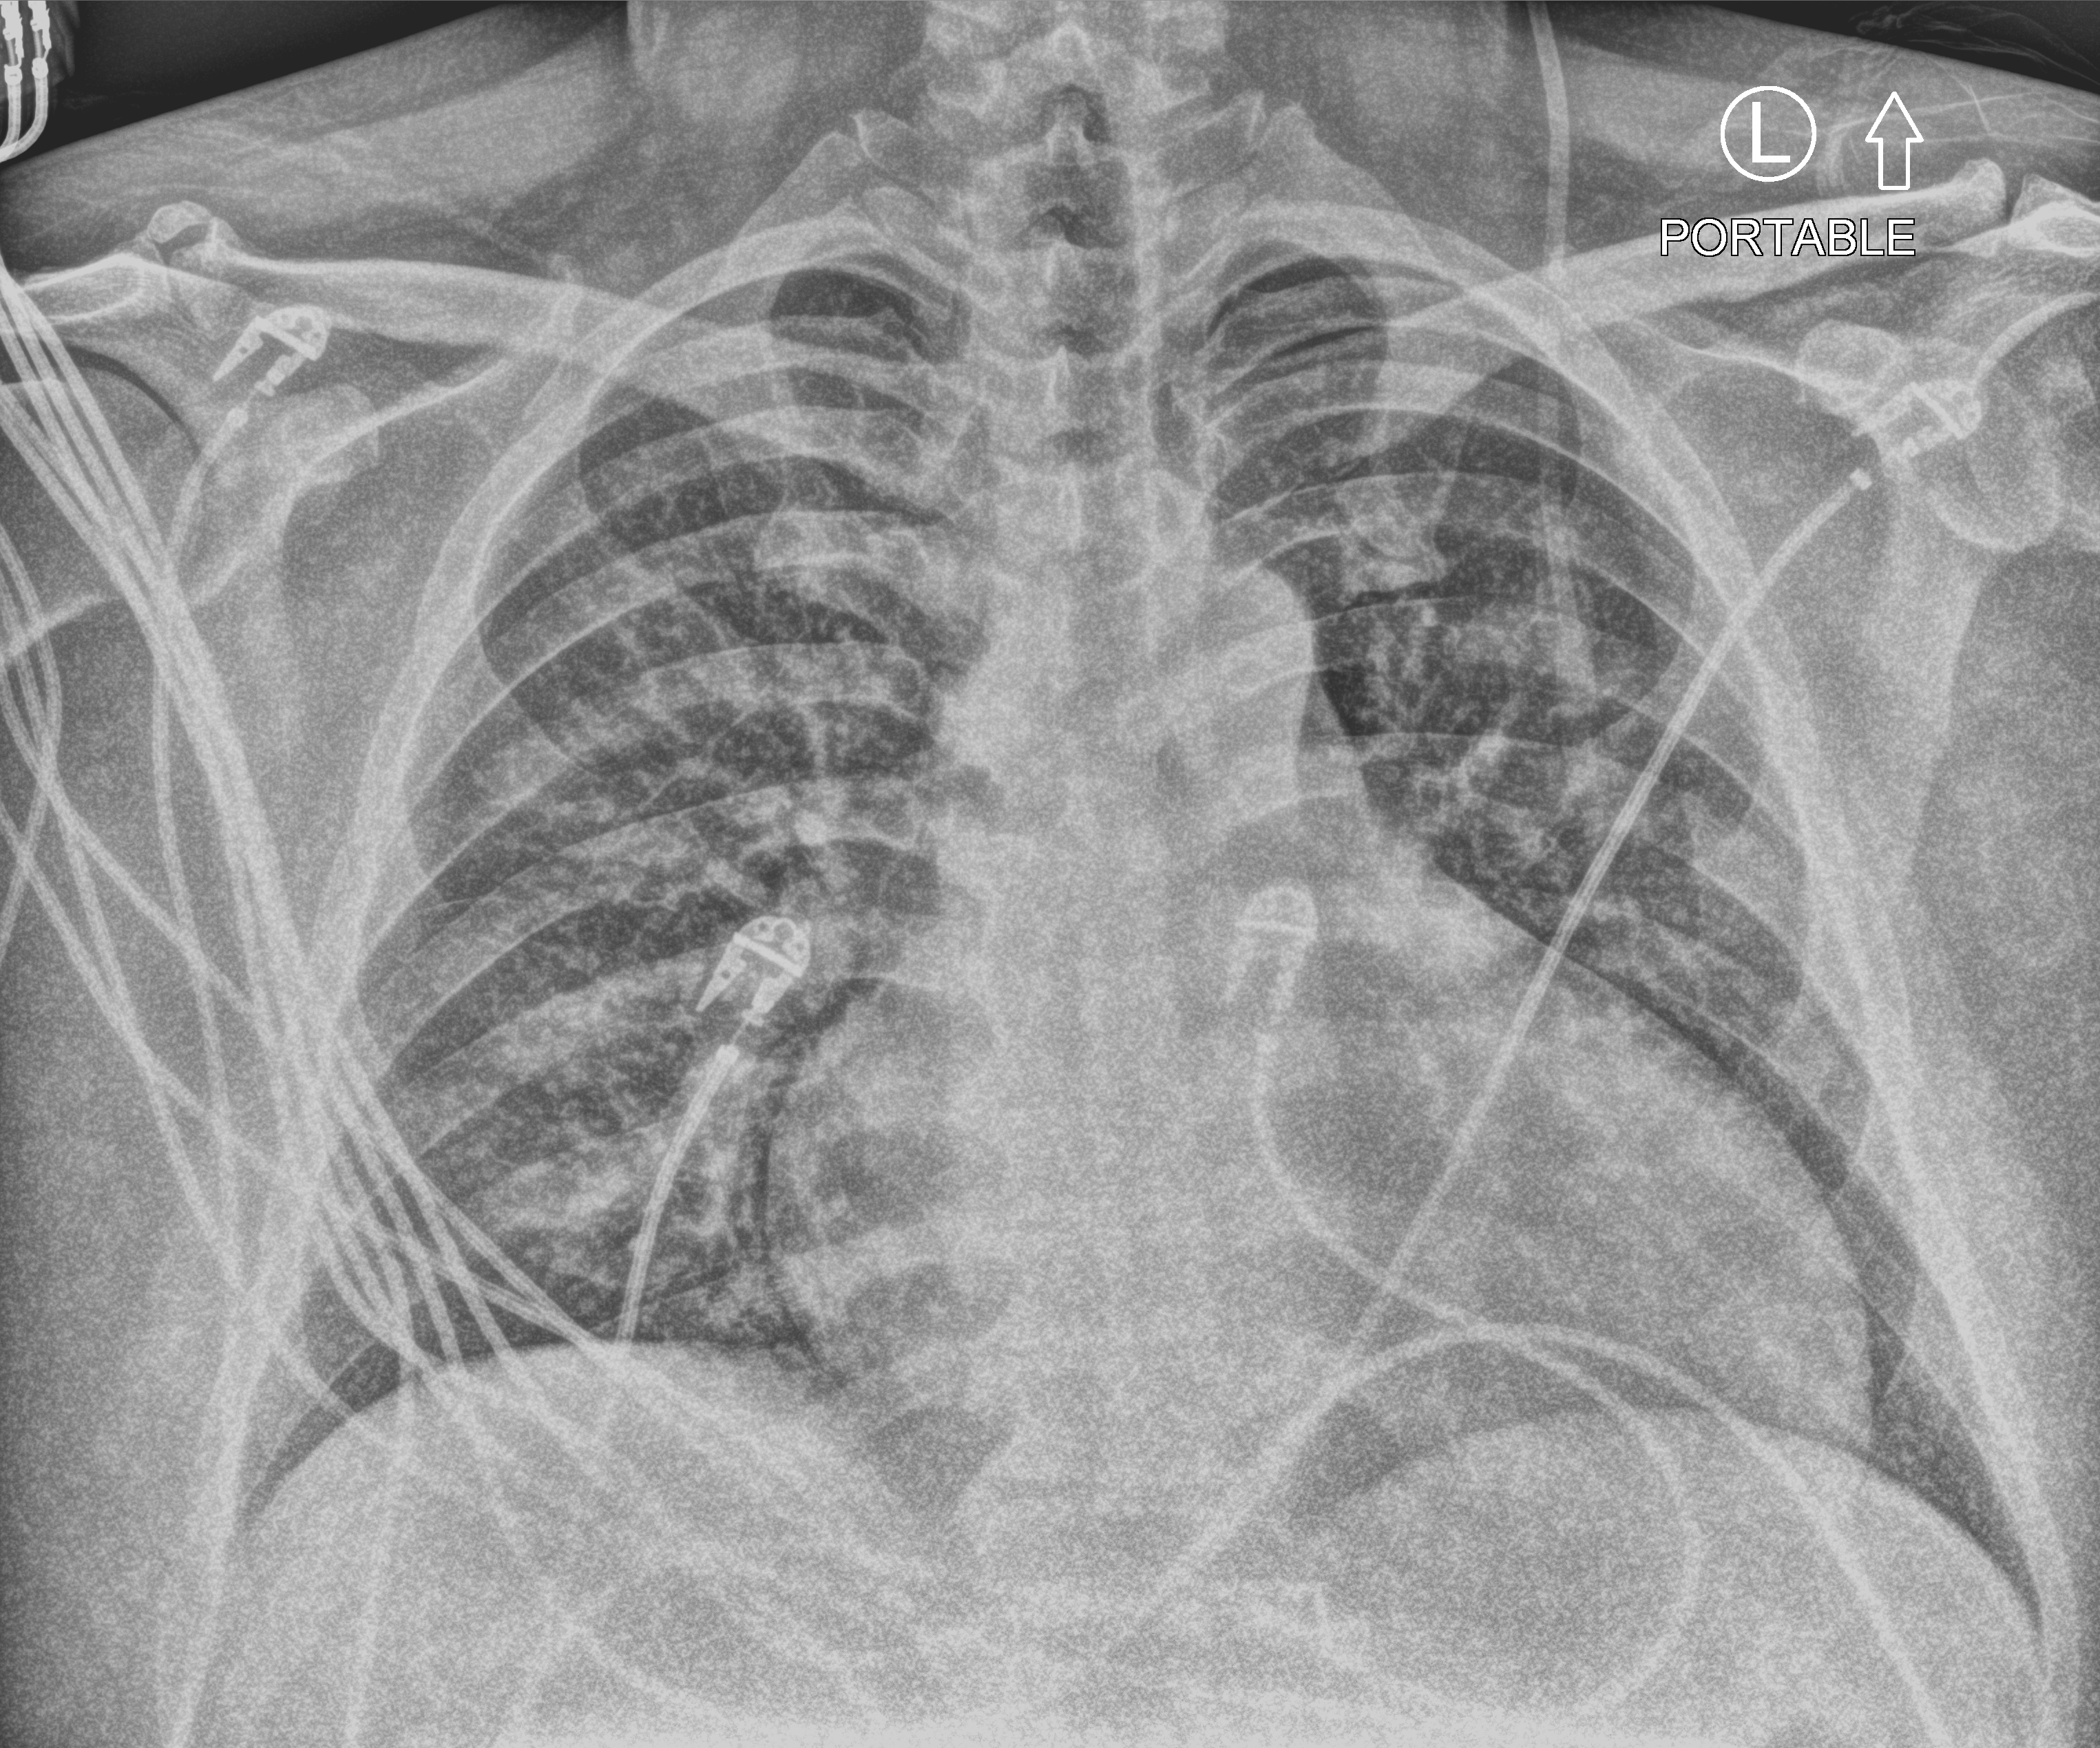
Chest X-ray (portable), anteroposterior (AP) projection. Patient hospitalised with COVID-19; male, aged 18–59 years.
From the hospital-stay record, not from the radiograph (when in the stay this image was taken is not recorded): length of hospital stay: 3 days; chronic kidney disease (admission record): no.